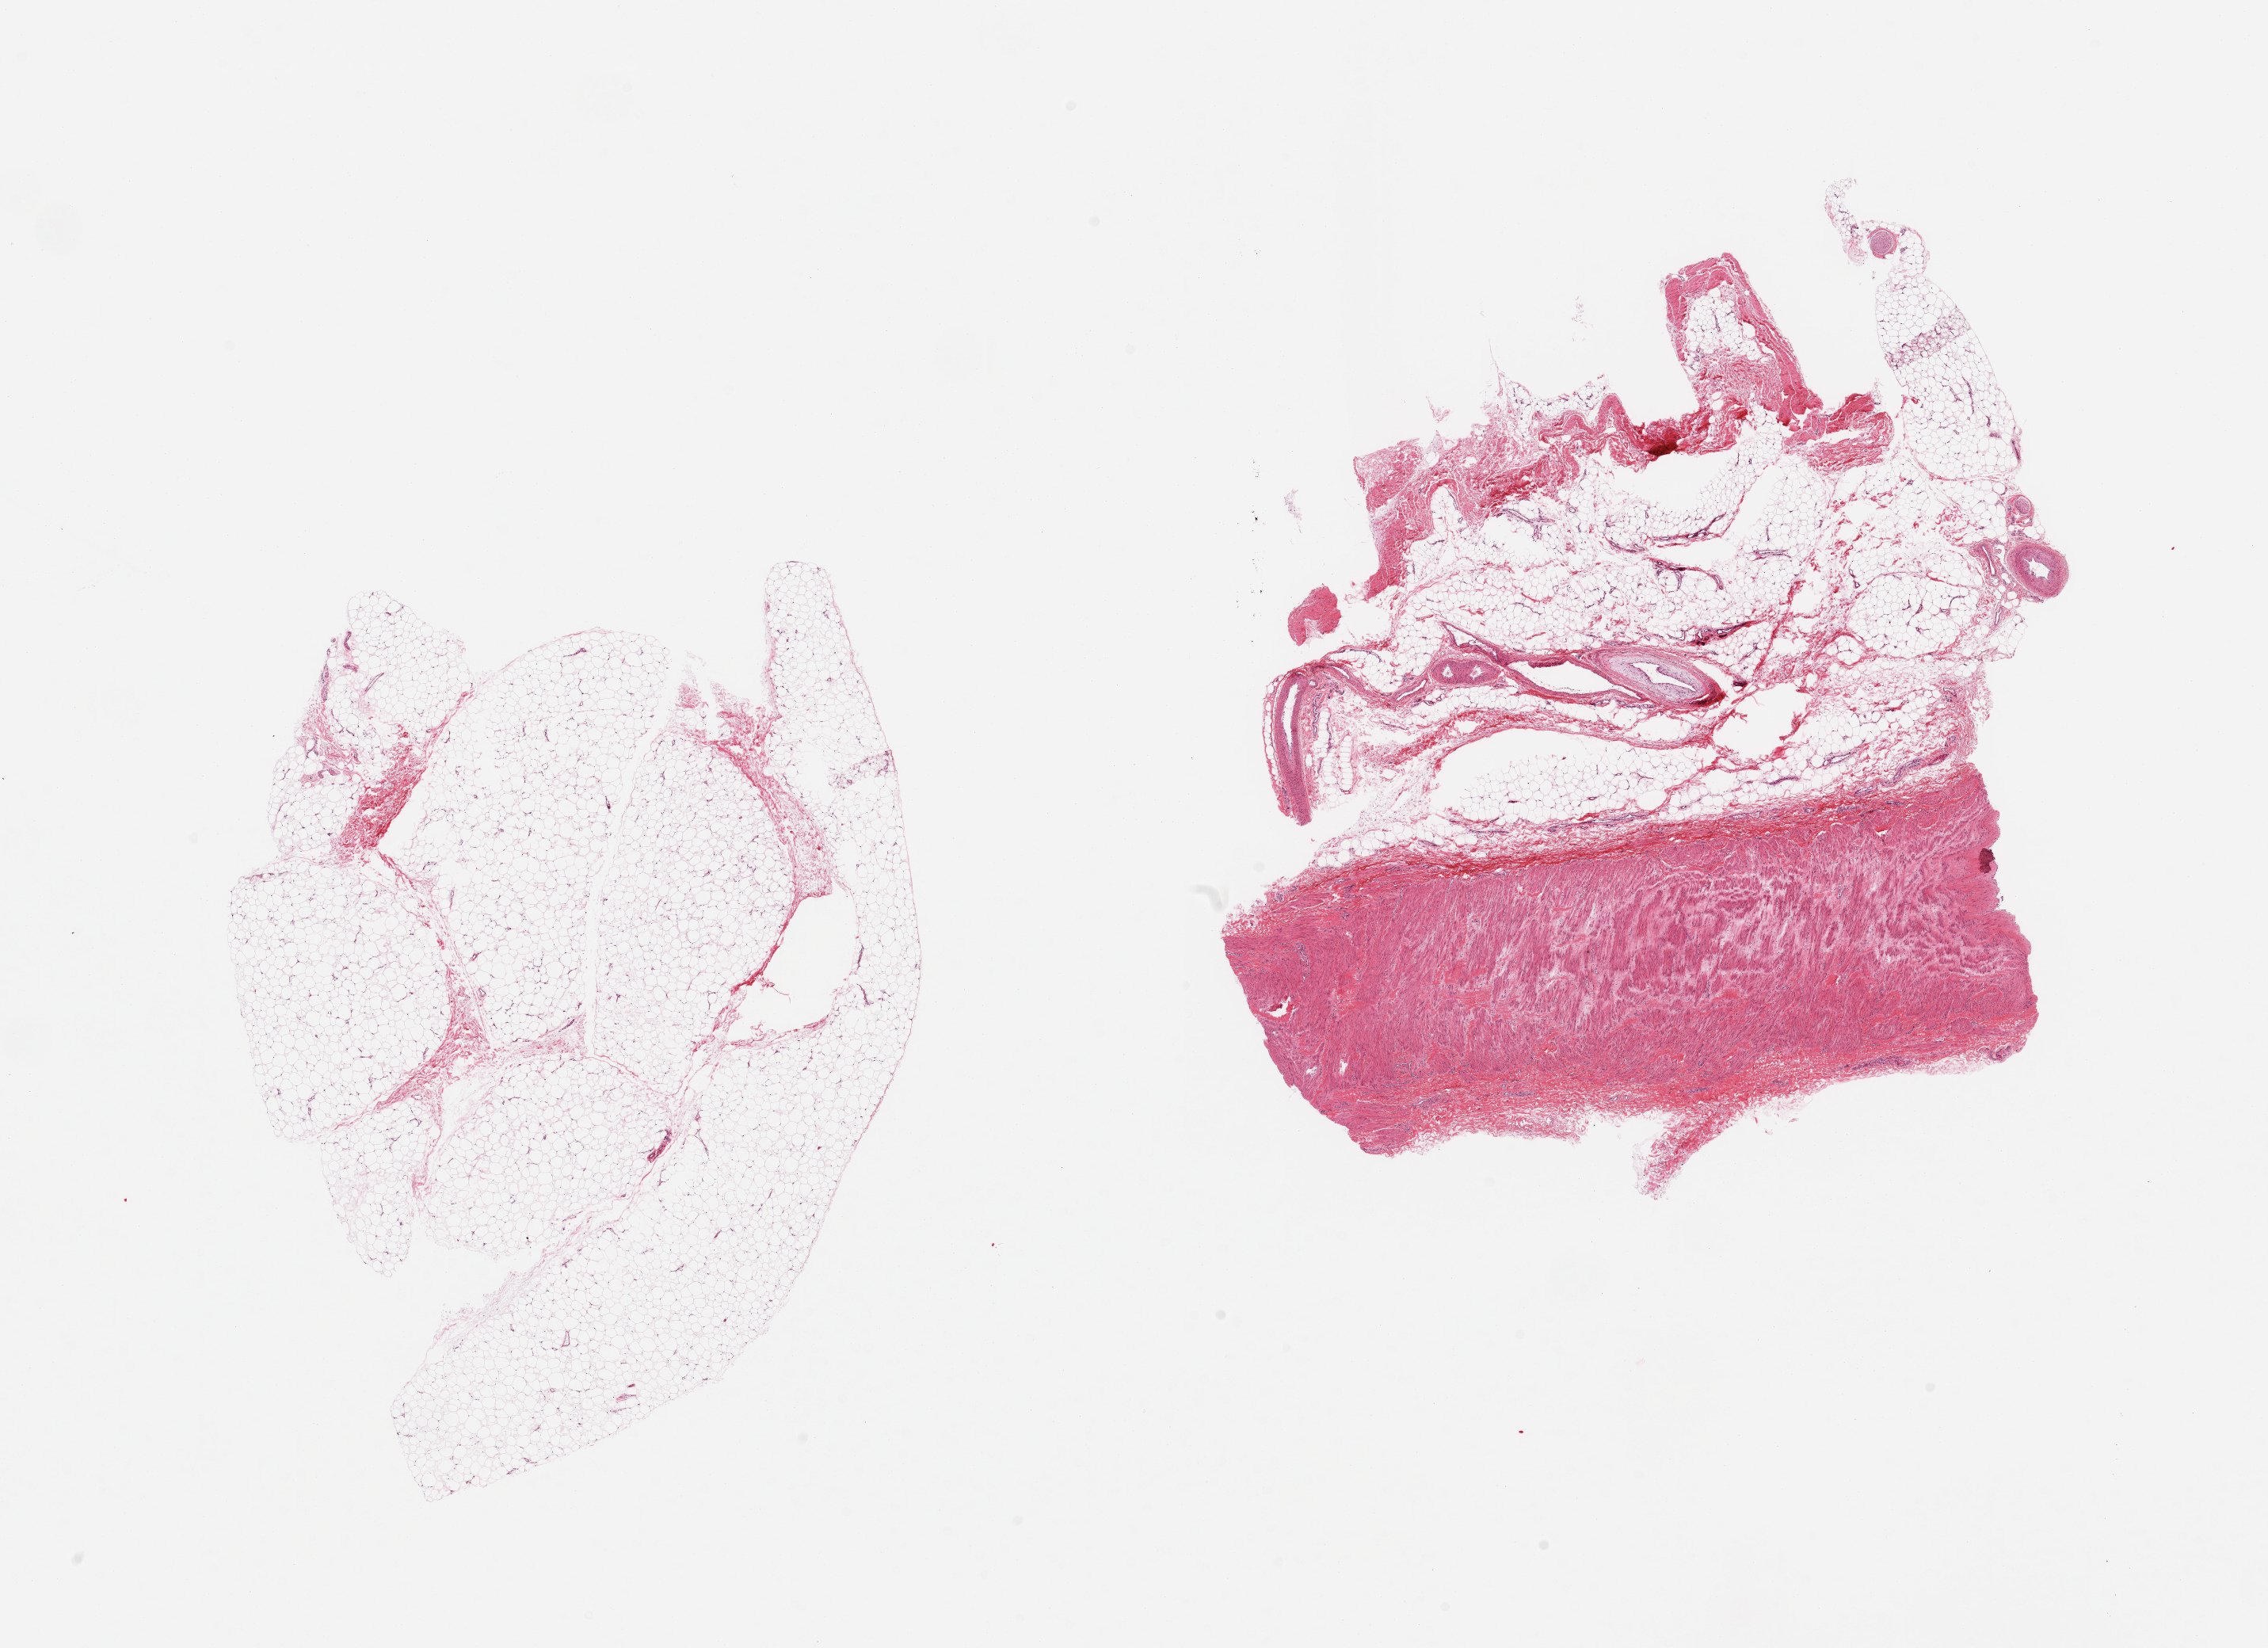
Whole-slide image, haematoxylin and eosin stain, whole scanned area (about 22.6 x 16.4 mm, from a 20x scan) shown as a low-resolution overview. PAXgene-fixed paraffin-embedded (PFPE) section. Sampled site (target tissue): adipose tissue. Donor tissue sample. Male donor.
- review note (as recorded): 2 pieces; mature adipose tissue with fibrovascular component and one piece with vessel wall up to ~3mm in thickness